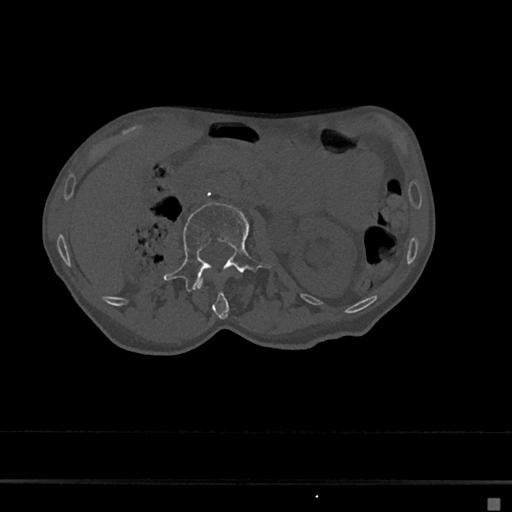
CT including the spine, one axial slice; reconstruction kernel Br40s/3; 120 kVp; bone window (W 1800 / L 400 HU); 512 × 512 image matrix, field of view 360 × 360 mm. Patient: female, 68 years. Case-level facts recorded for this patient, not image findings: primary cancer: renal.
Outlined on this slice (semi-automatic segmentation, software-assisted and operator-edited):
- L1 vertebra: bounding box [x1, y1, x2, y2] px = [197, 272, 240, 319]
- L2 vertebra: [163, 202, 272, 292]